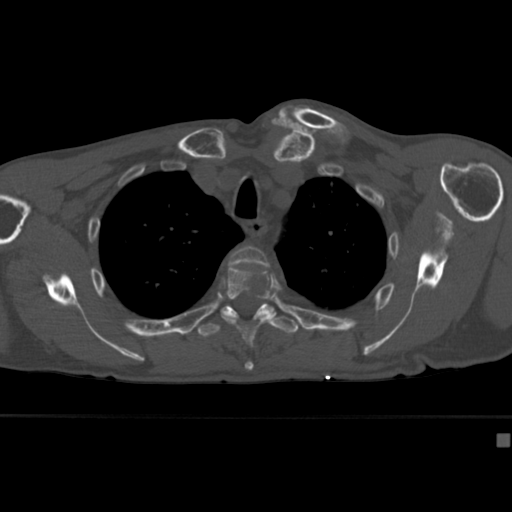
CT including the spine, one axial slice; position 319 of 430 along the scan axis; bone window (W 1800 / L 400 HU); 512 × 512 image matrix, field of view 337 × 337 mm. Patient: male, 64 years. From the clinical record (not read from this slice): primary cancer: uterus; vertebrae with lytic lesions (as recorded): T1, T4, T5, T7, L5.
Structures marked on this image (semi-automatic segmentation, software-assisted and operator-edited):
- T3 vertebra: bounding box <228,246,270,269> (left, top, right, bottom; pixels)
- T4 vertebra: <213,268,320,371>
- T5 vertebra: <198,304,299,337>